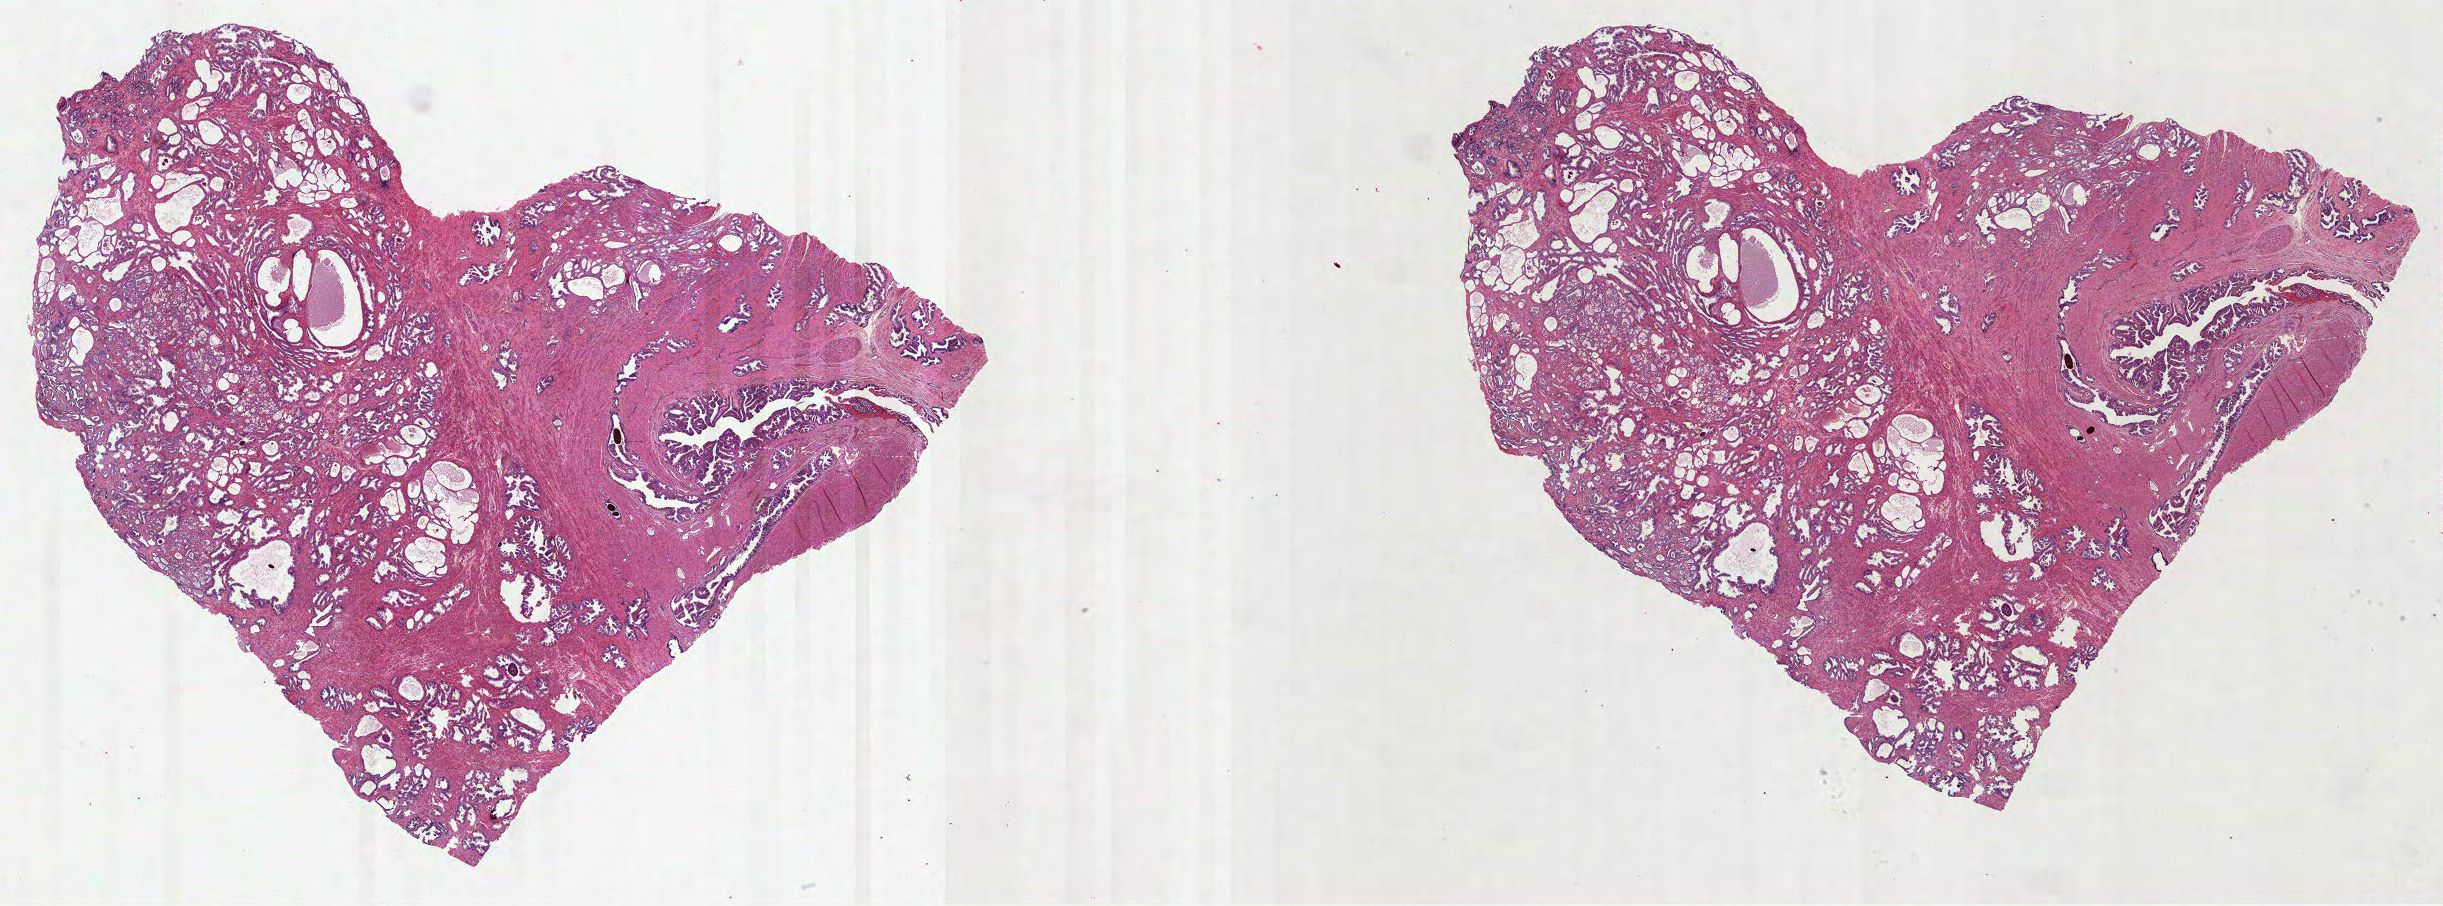
Whole-slide histology image, H&E — shown as a low-resolution overview of the whole scanned area (about 39.4 x 14.6 mm, from a 40x scan); formalin-fixed paraffin-embedded (FFPE) diagnostic section; prostate, primary tumour sample. Male patient; age at initial diagnosis 49 years. Gleason score: 7 (3+4).
Diagnosis: Acinar cell carcinoma. Laterality: bilateral.